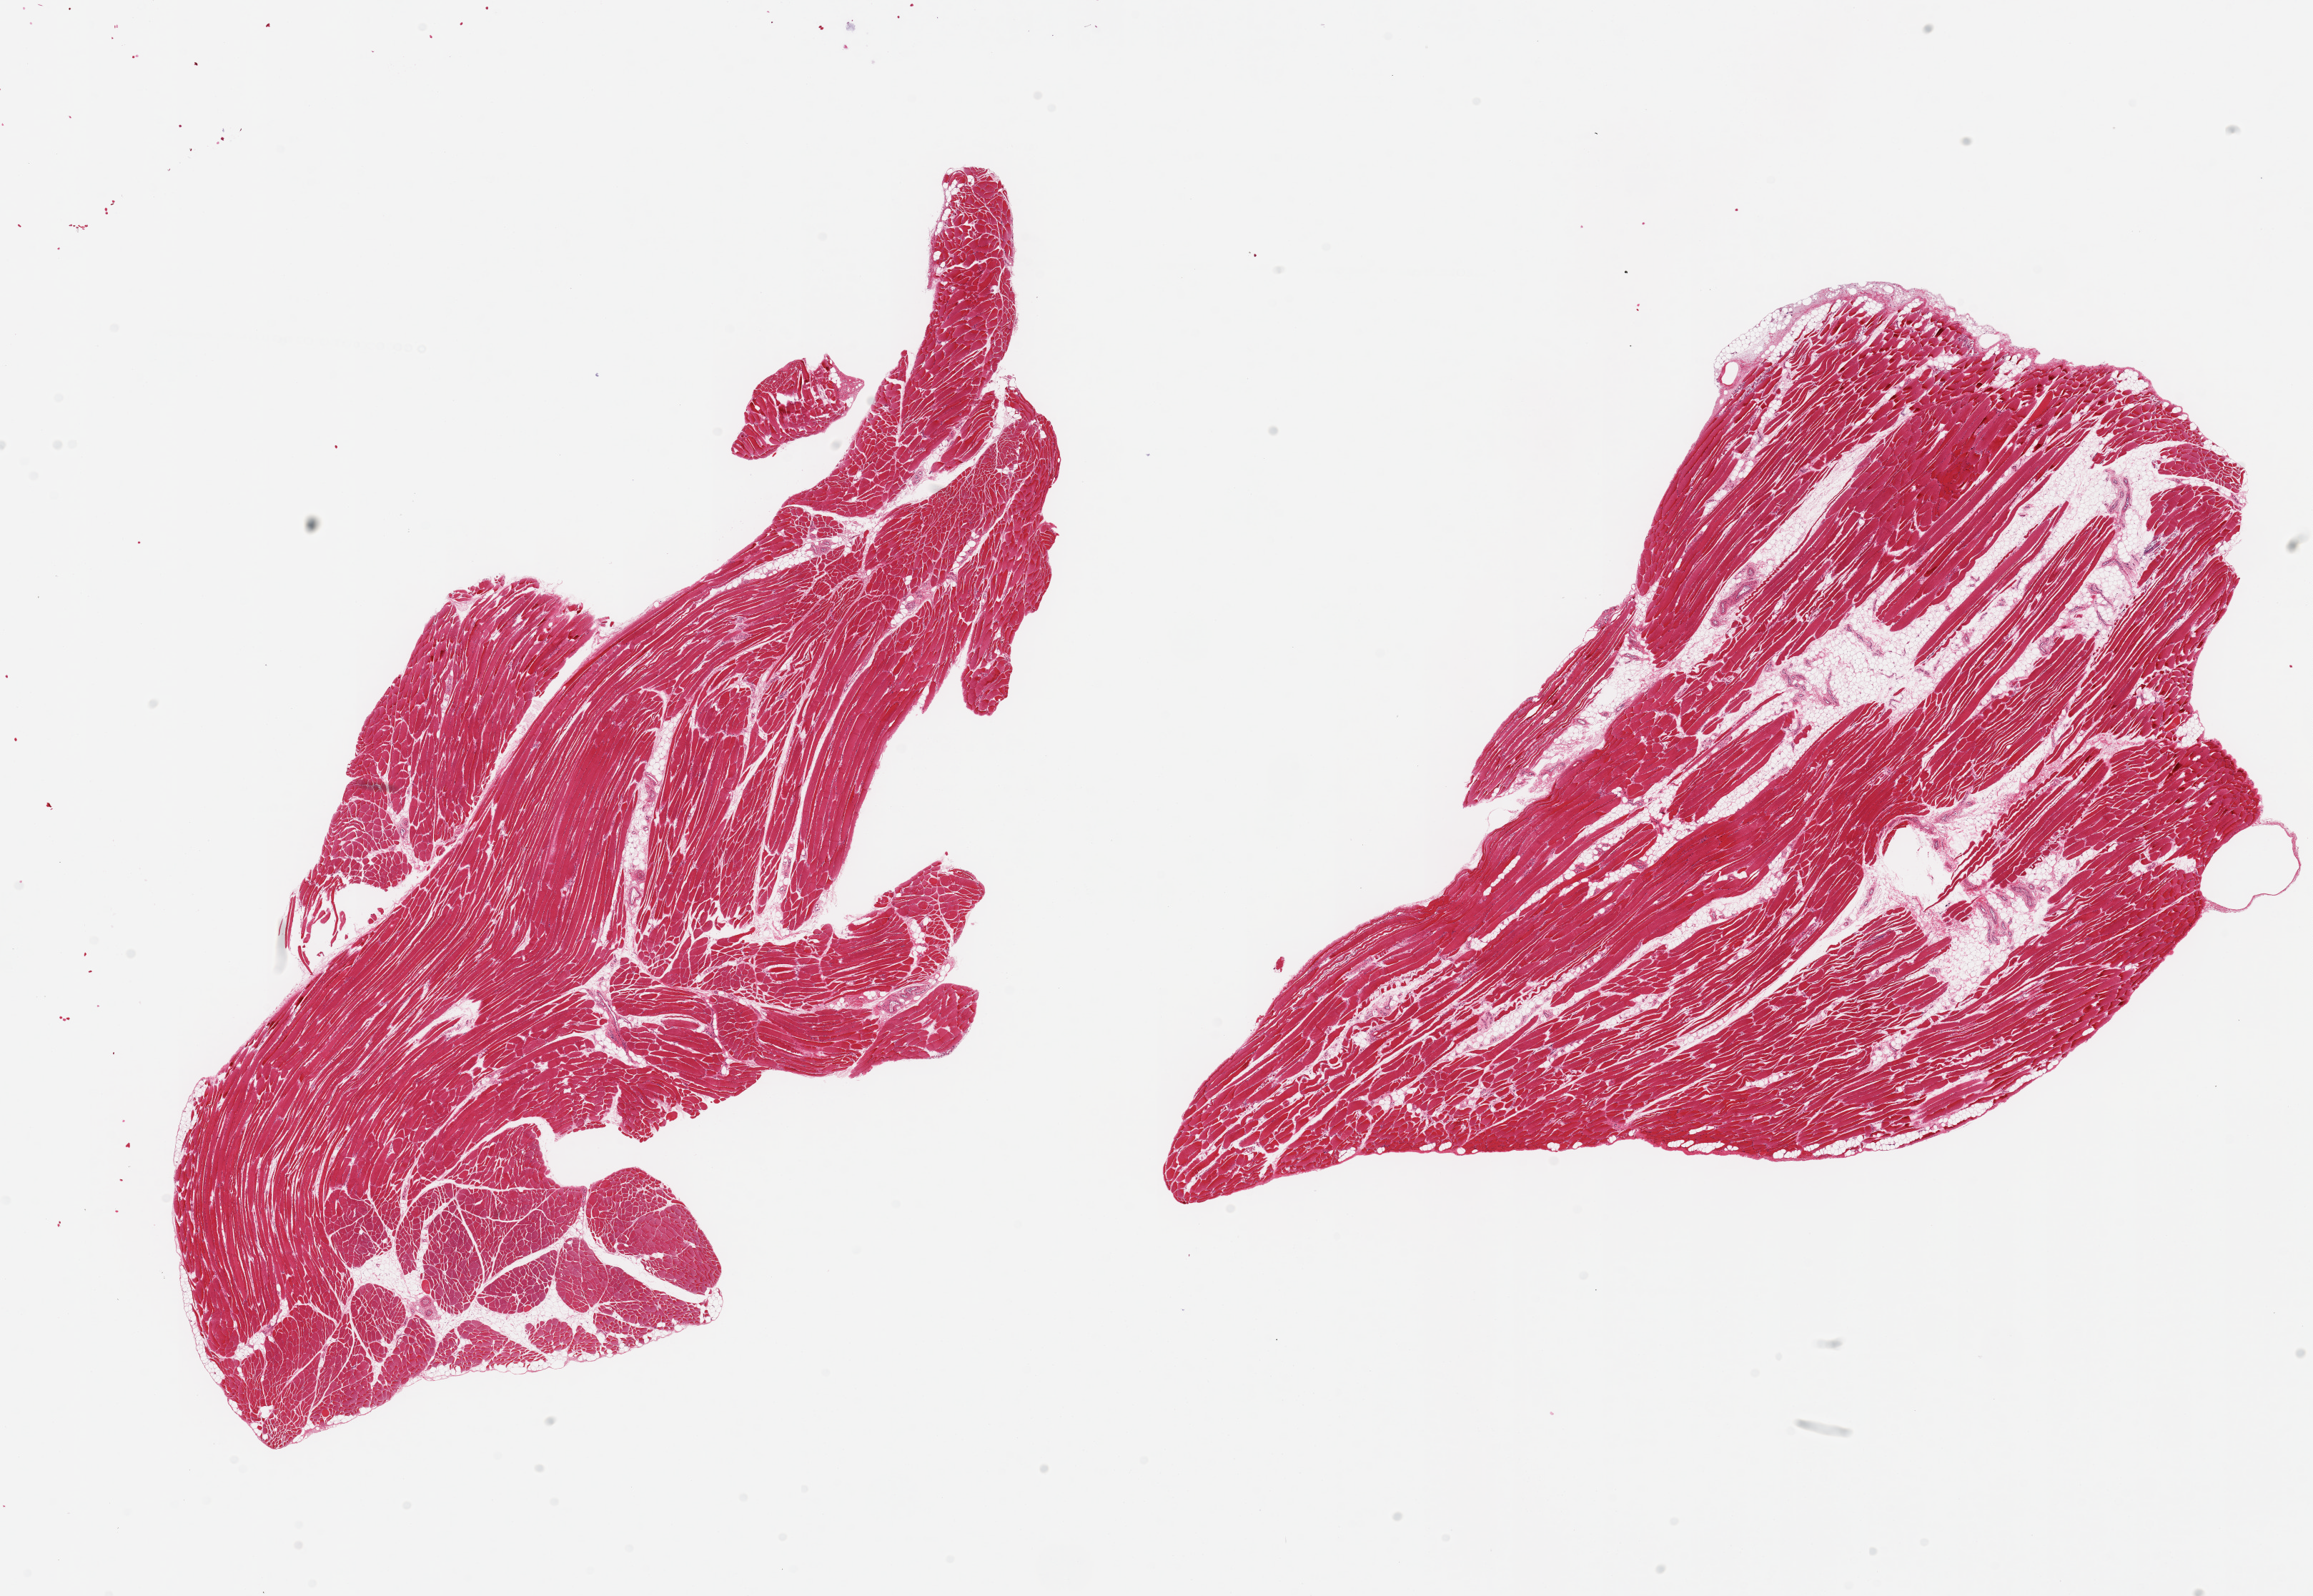
Whole-slide image, hematoxylin and eosin (H&E) stain — low-resolution overview of the scanned area, about 25.6 x 17.7 mm. PAXgene-fixed paraffin-embedded (PFPE) section. Target tissue: skeletal muscle. Tissue donor sample. Donor sex: male.
Pathologist's review note for this sample: 2 pieces; ~3% and 10% internal fat, rare atrophic fibers.